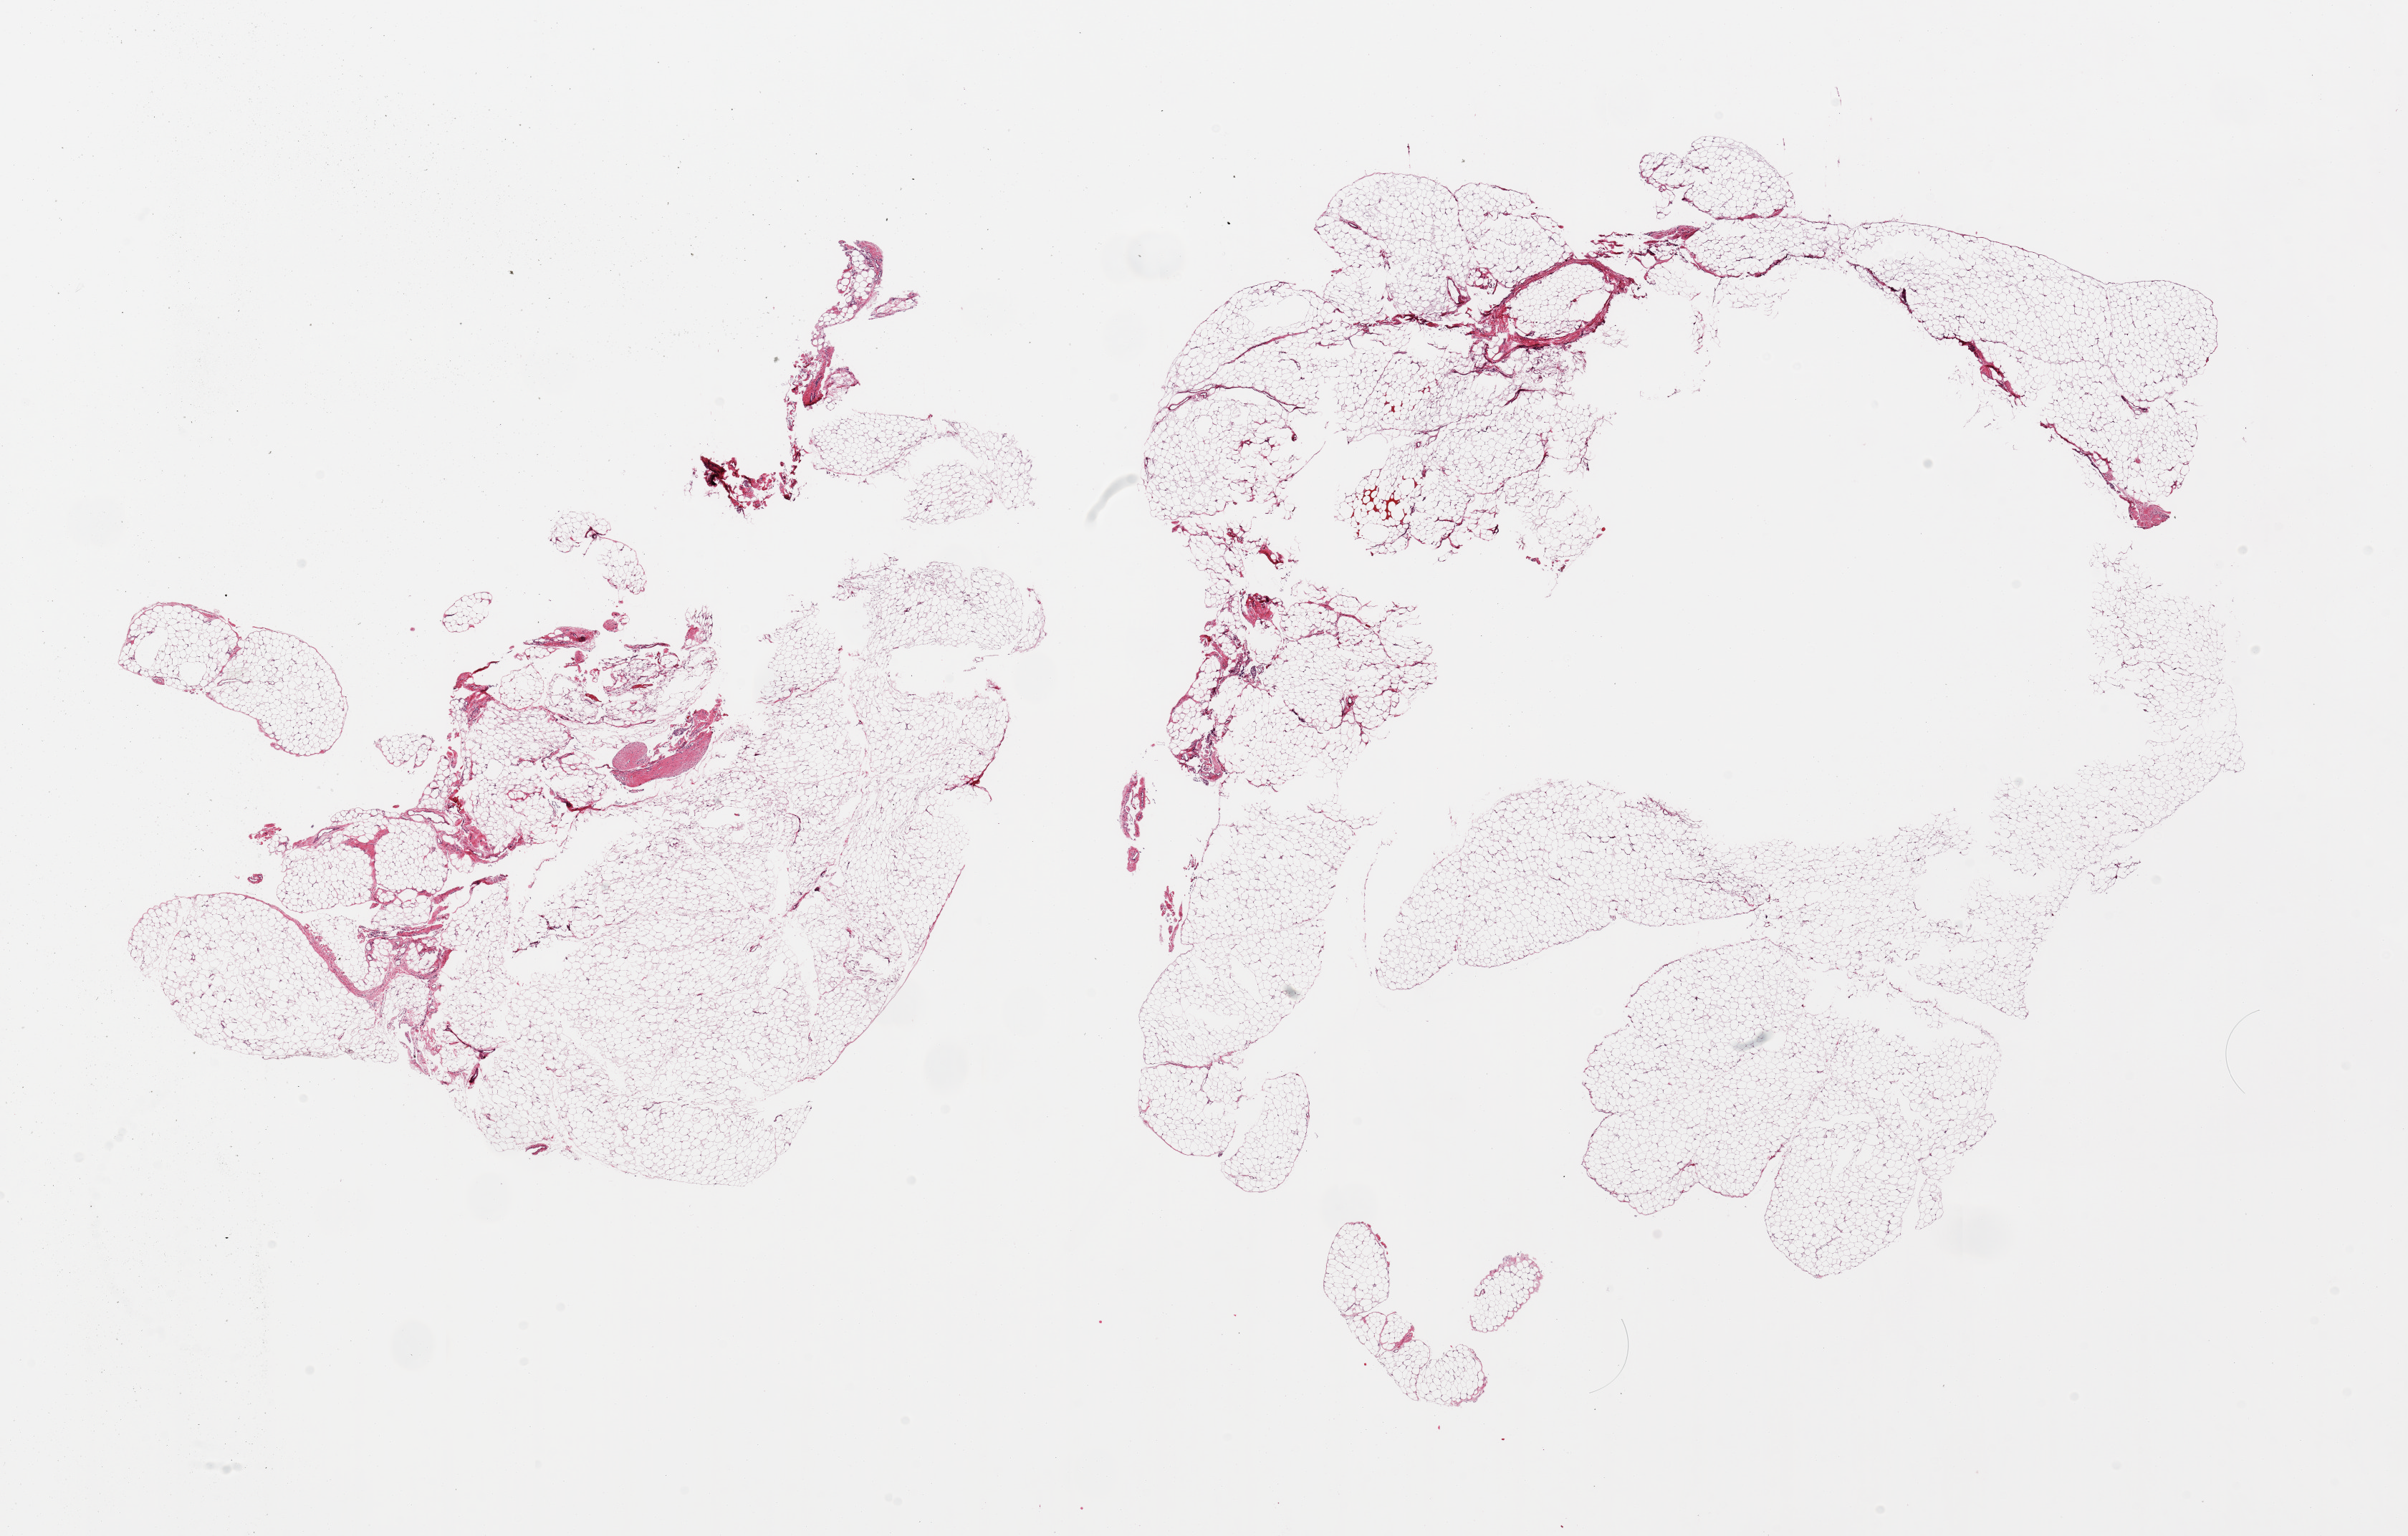
Digitized hematoxylin and eosin (H&E)-stained section, shown as a low-resolution overview of the whole scanned area (about 26.6 x 17.0 mm), PAXgene-fixed paraffin-embedded (PFPE) section, sampled site (target tissue): omentum, tissue donor sample. Donor sex: male.
Reviewer comment on this tissue sample: 2 pieces., minimal fascia/ vasular elements.